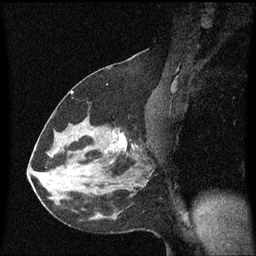
Breast MRI (dynamic contrast-enhanced), one sagittal slice; position 34 of 60 along the scan axis; dynamic contrast-enhanced series, image 2 of 3 at this slice position (ordered by acquisition); 1.5 T; TE 4.2 ms, TR 8.4 ms; 2 mm slice thickness; 256 × 256 image matrix, field of view 200 × 200 mm. Female patient, age 37 years. From the clinical record (not read from this slice): setting: breast cancer imaged before/during neoadjuvant chemotherapy; receptor status: HR-positive, HER2-negative.
Structures marked on this image (semi-automatic segmentation, software-assisted and operator-edited):
- analysis volume of interest (the breast-tissue region the enhancement analysis was run in; not a lesion): bounding box [x1, y1, x2, y2] px = [95, 108, 153, 171]
- tumour enhancement mask (voxels above the 70 % enhancement threshold inside the analysis volume of interest): [119, 132, 128, 149]